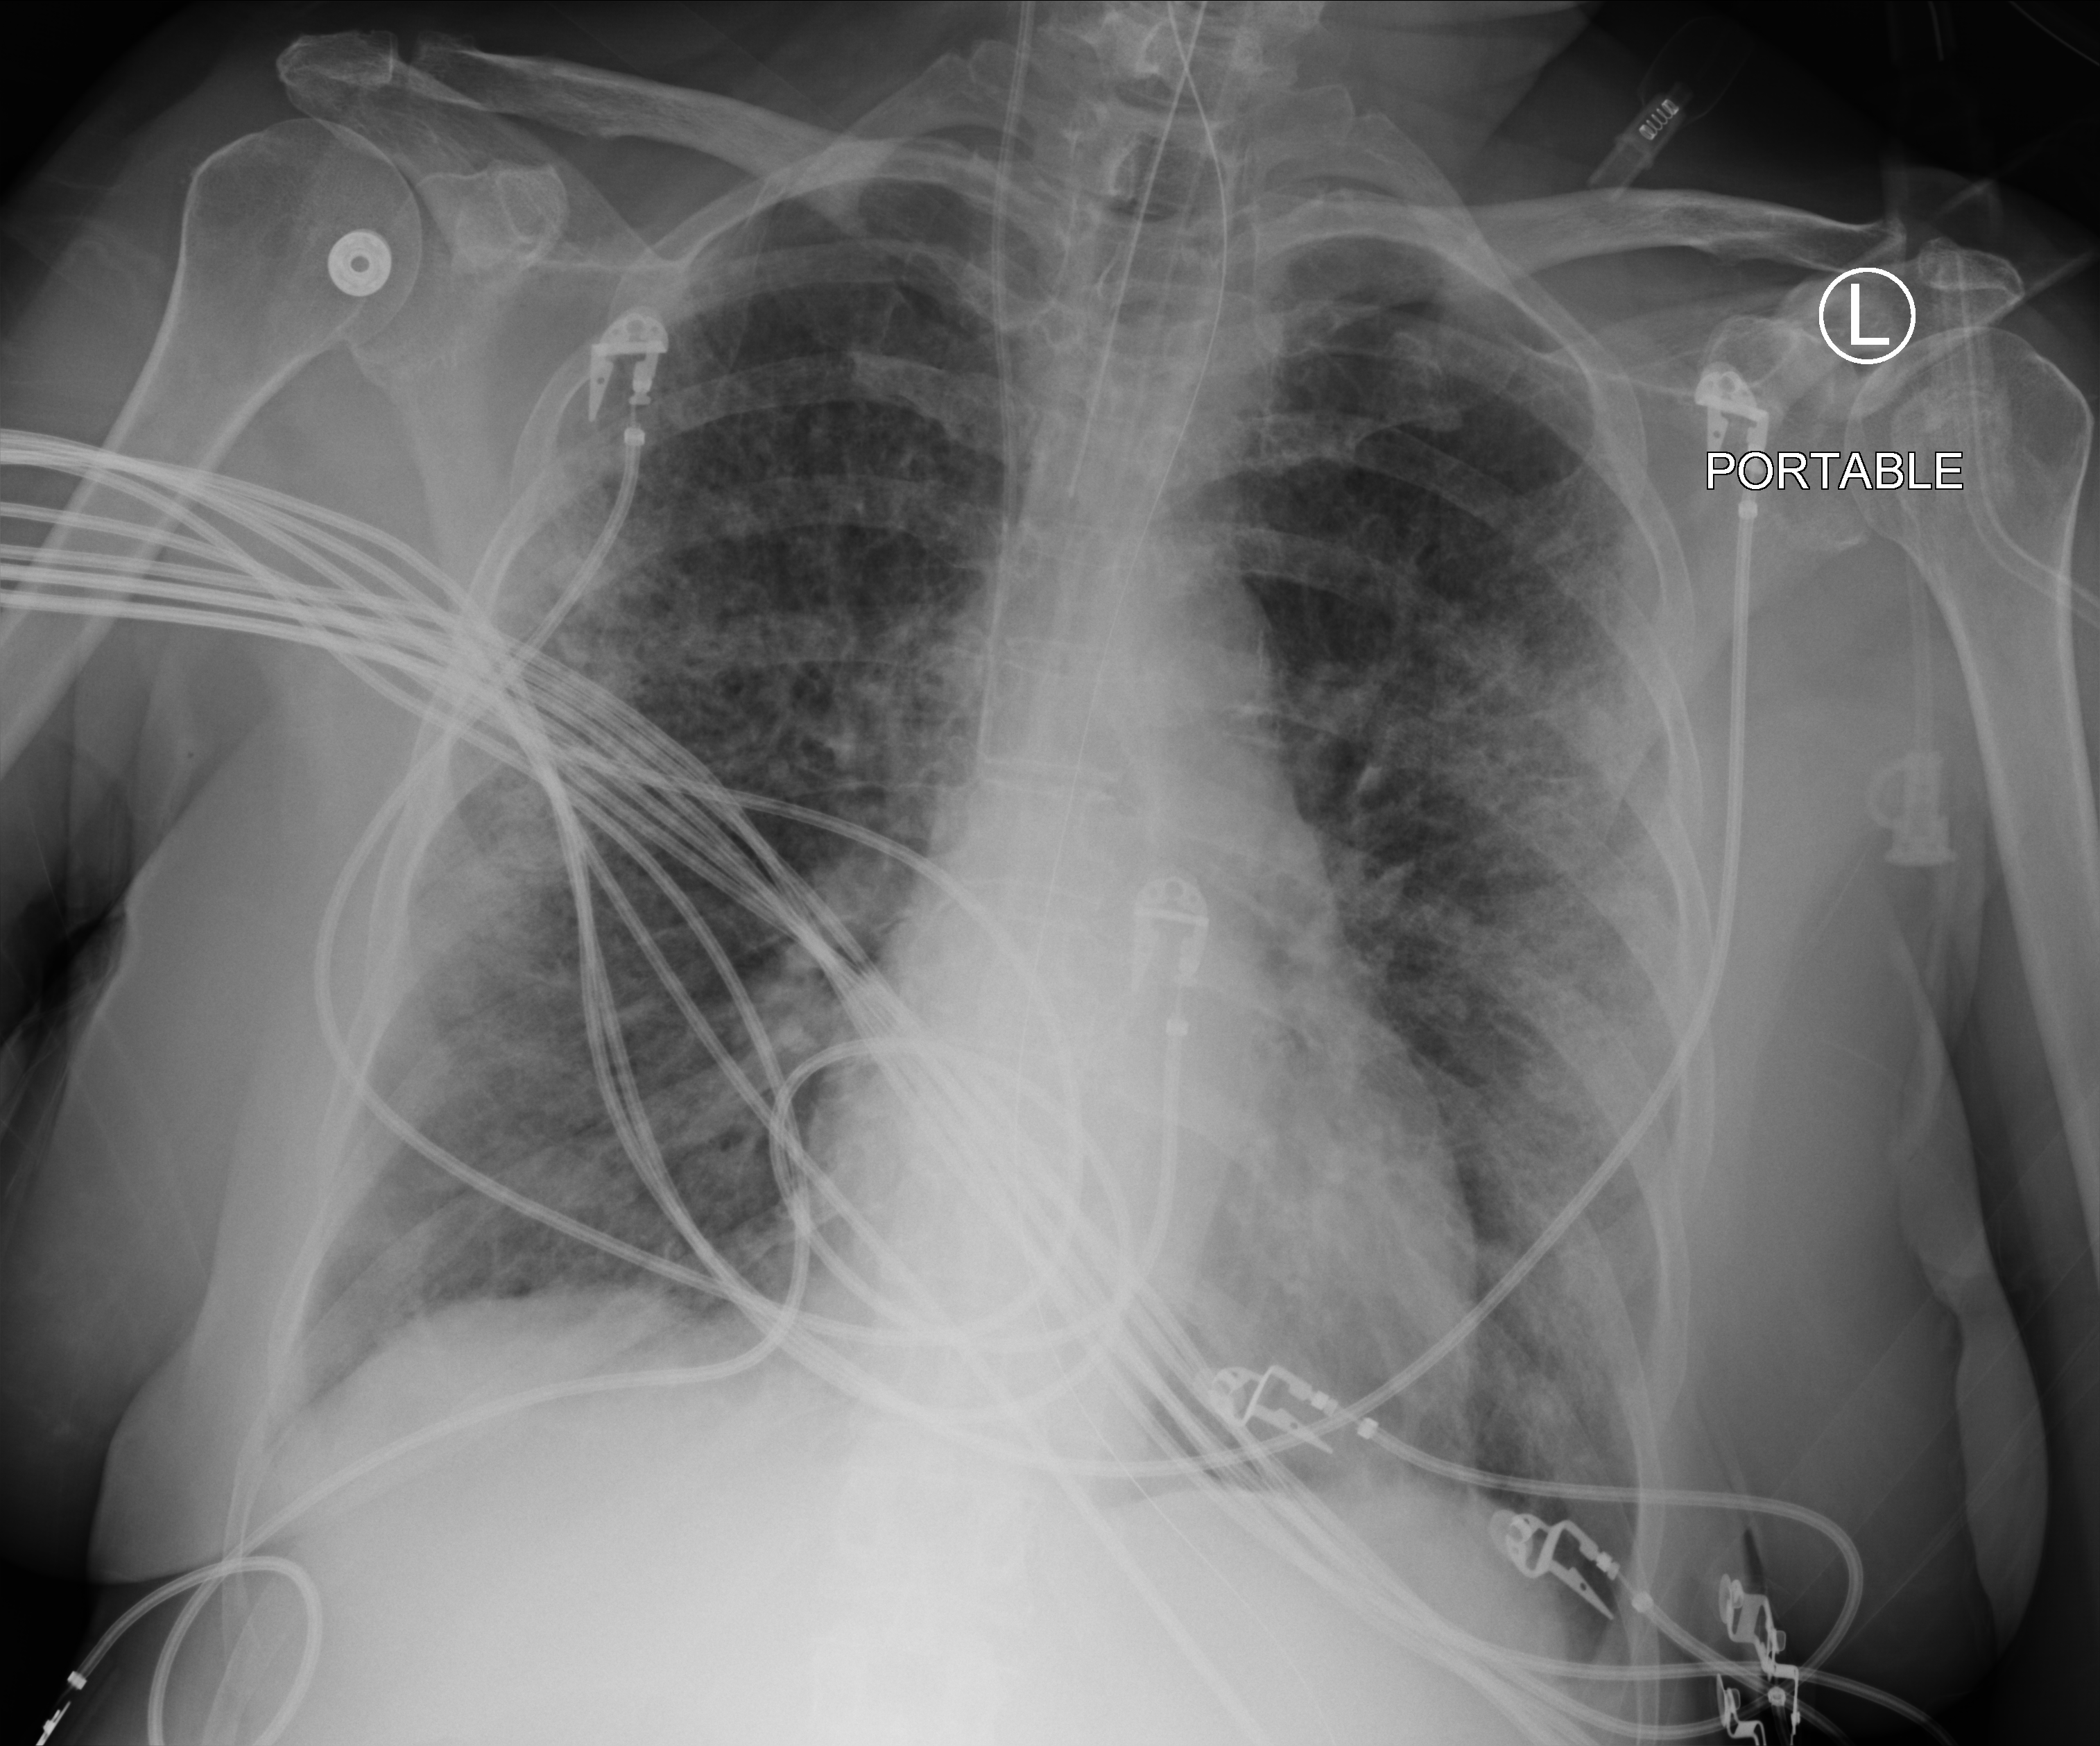
Chest X-ray (portable). Patient hospitalised with COVID-19; female, aged 60–74 years.
Admission-level facts for this patient (not findings on this image; timing relative to this image not recorded): length of hospital stay: 15 days; hypertension (admission record): yes.